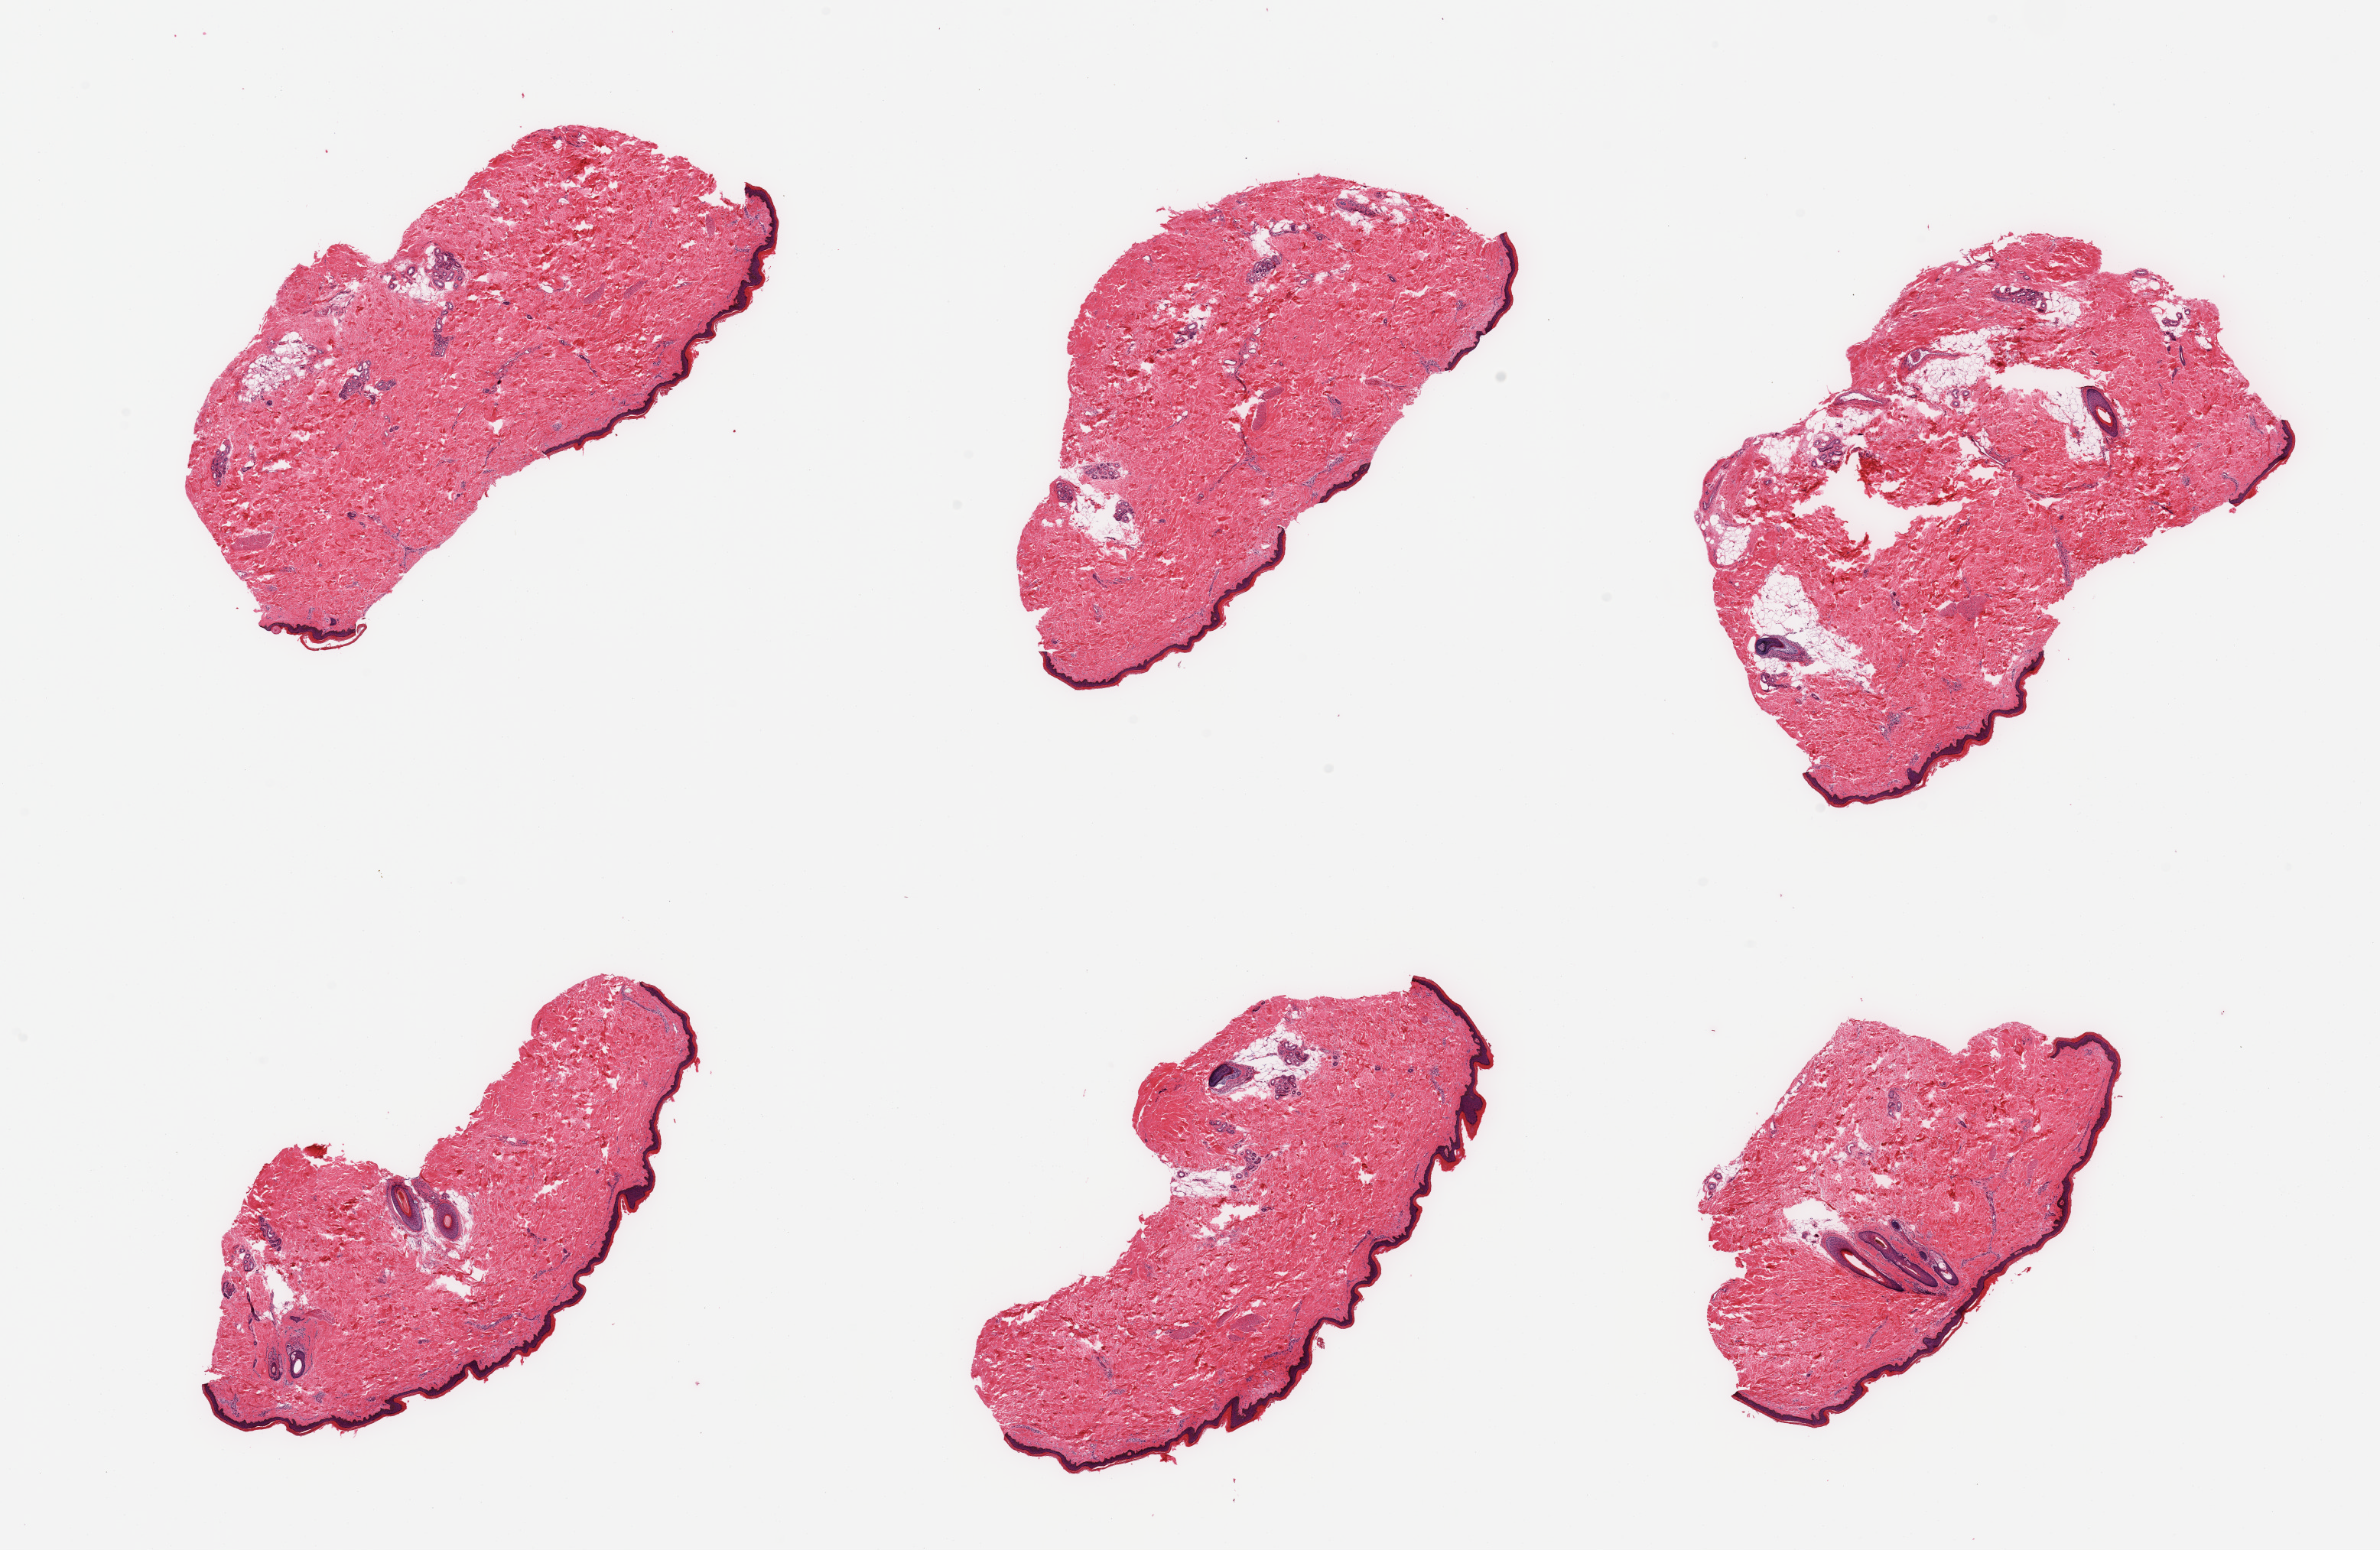
Digitized haematoxylin and eosin-stained section, a low-resolution overview of the entire scanned area, about 24.6 x 16.0 mm. PAXgene-fixed paraffin-embedded (PFPE) section. Sampled site (target tissue): skin of lower leg. Tissue donor sample. Donor: male.
Reviewer comment on this tissue sample: 6 pieces; ; epidermis ~41 microns thick; 5% to 20% of periadnexal (internal) fat; a few hair follicles.